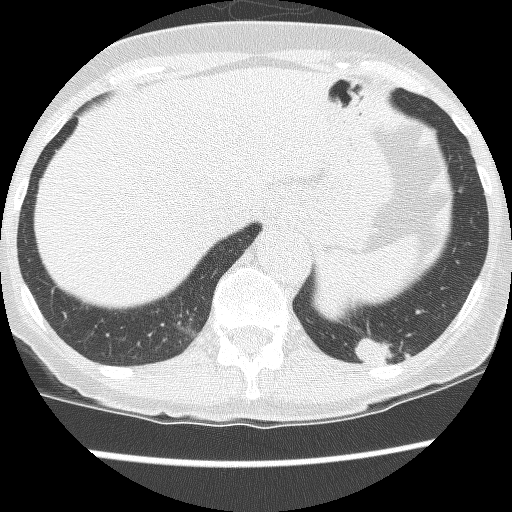
Low-dose screening chest CT, axial slice; third screening round (two years after baseline); lung window (W 1500 / L -600 HU); 120 kVp; slice 106 of 130 in the series; 512 × 512 image matrix, field of view 290 × 290 mm. Female participant, aged 61 years at enrolment. Current smoker at enrolment.
• Expert reader's lesion annotation, box from (x=336, y=296) to (x=438, y=385) px.
• The screening reader recorded 2 non-calcified nodules or masses ≥4 mm on this exam; which of them this box marks is not recorded.